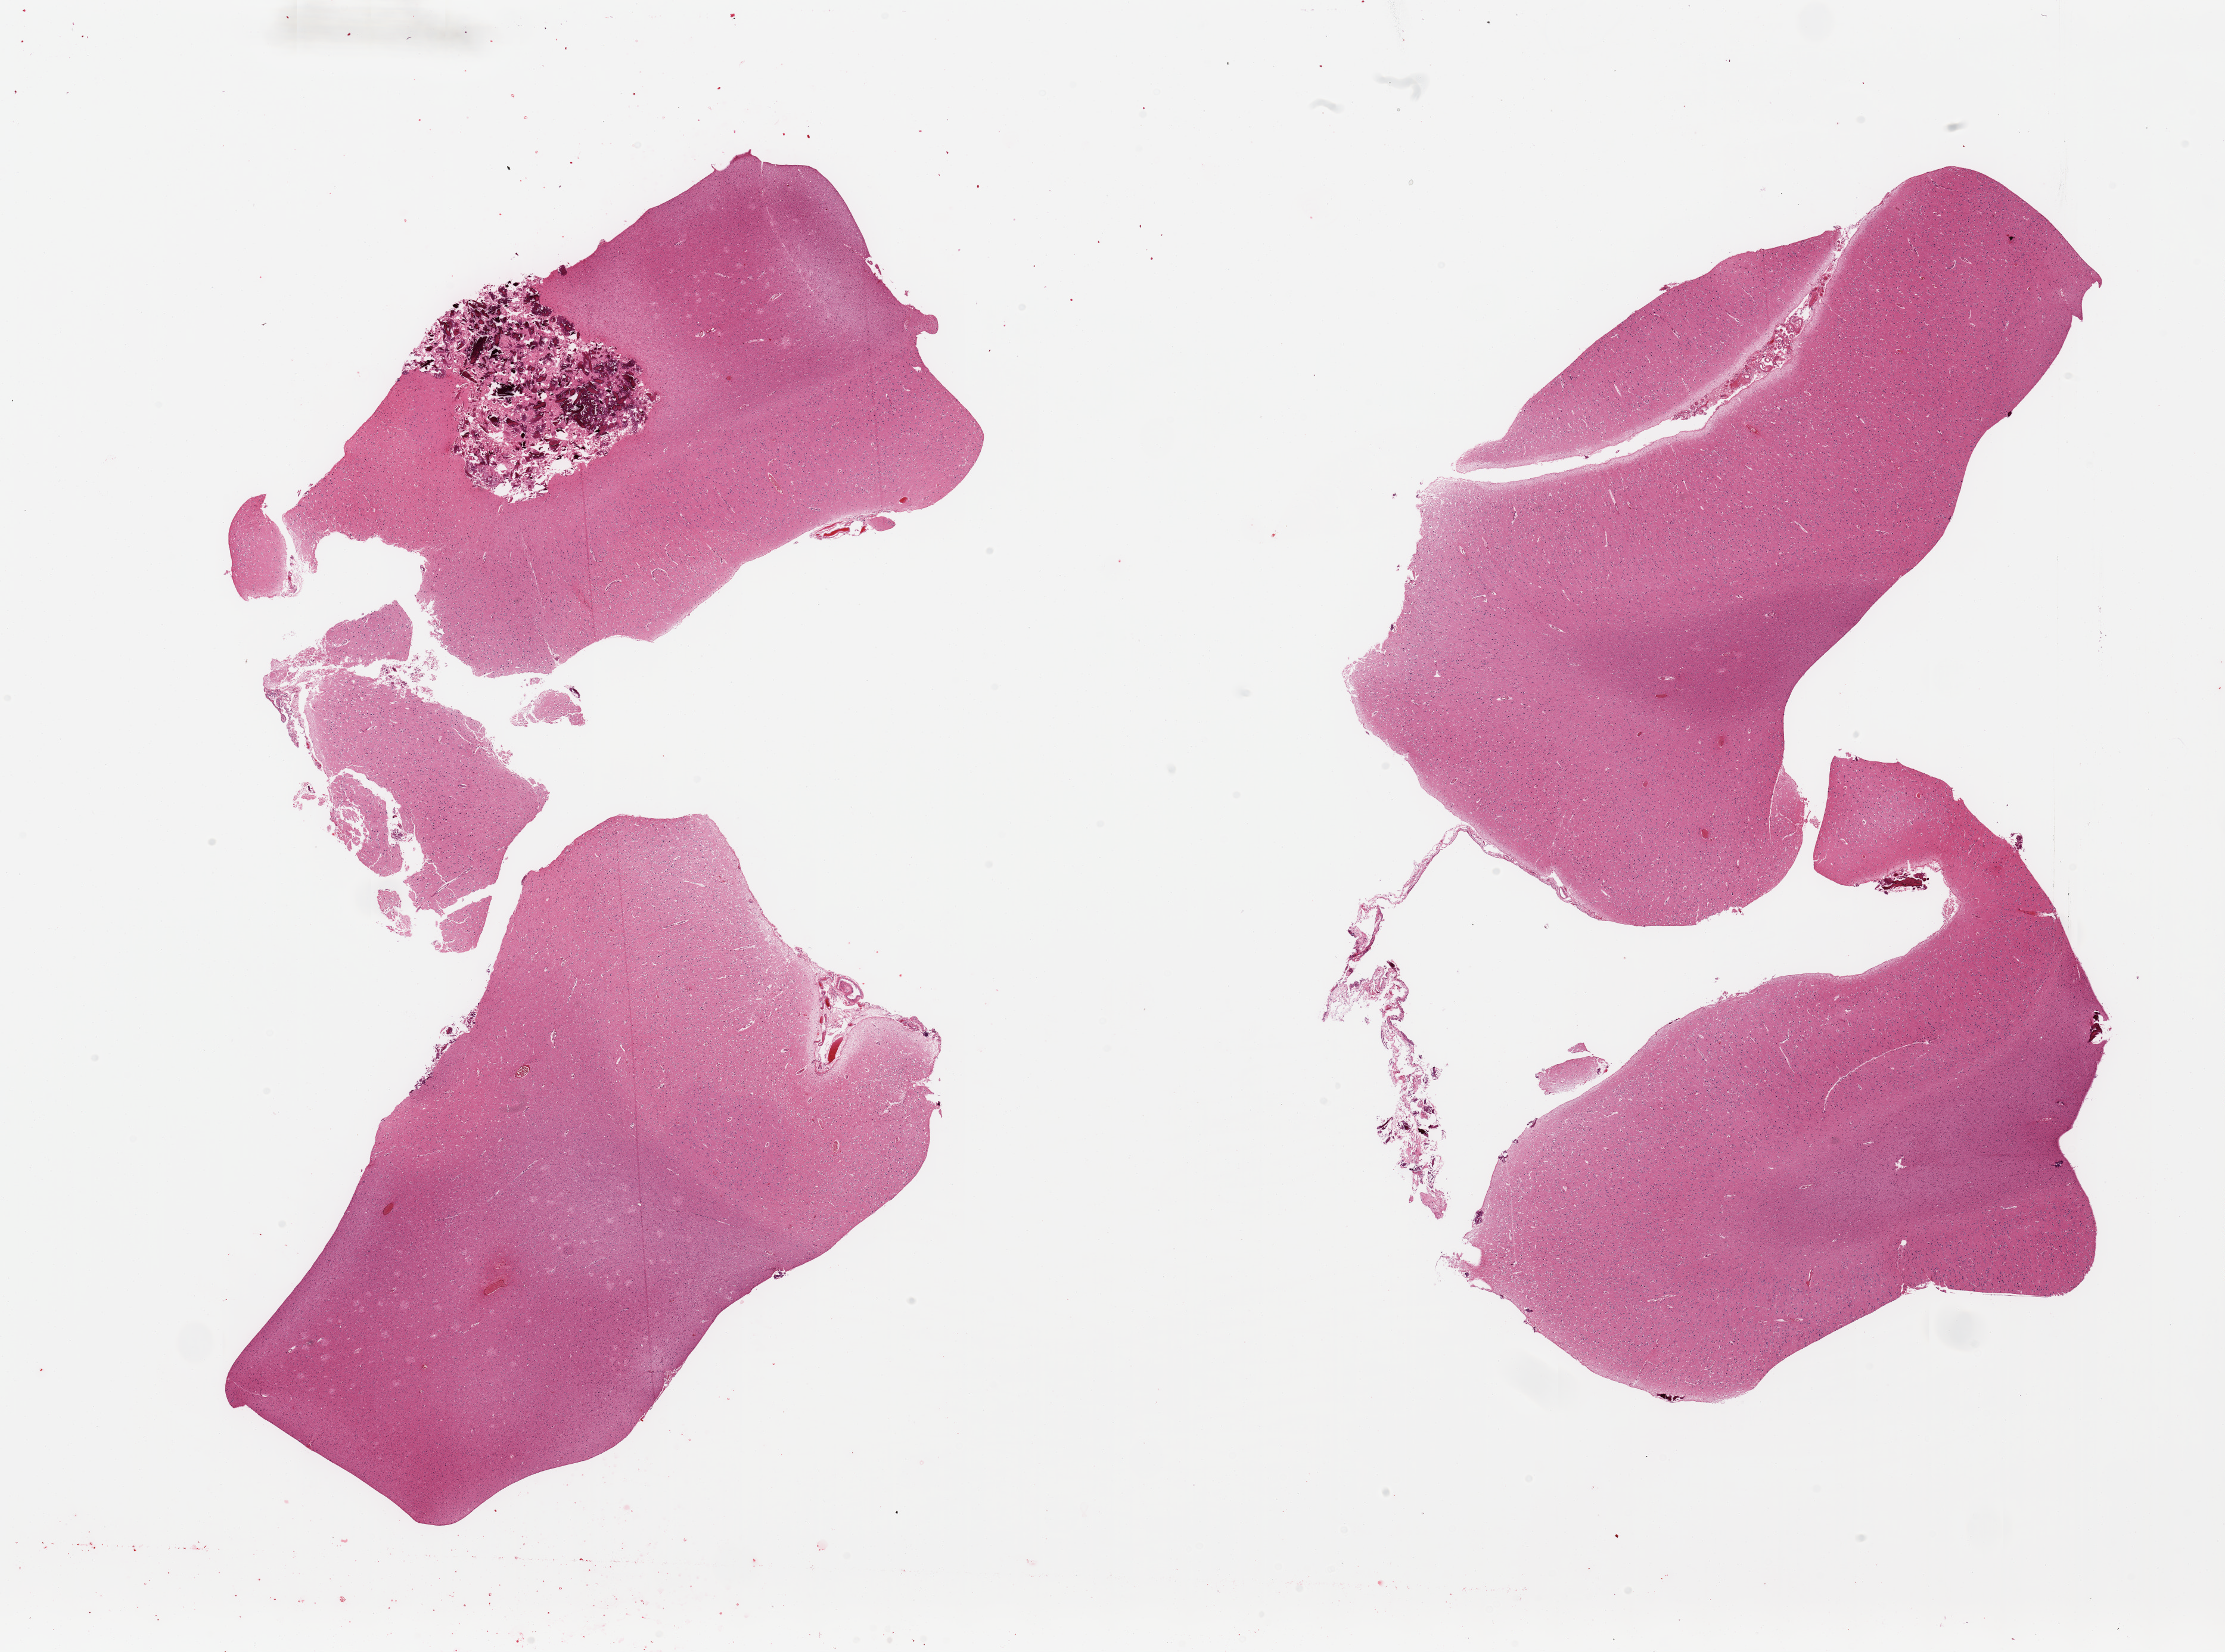
Digitized haematoxylin and eosin-stained section, brightfield, low-resolution overview of the scanned area, about 29.5 x 21.9 mm. PAXgene-fixed paraffin-embedded (PFPE) section. Sampled site (target tissue): cerebral cortex. Tissue donor sample.
Pathologist's review note for this sample: 4 pieces; 2.5x2.5mm focus of bone and meningeal debris embedded in cortex.